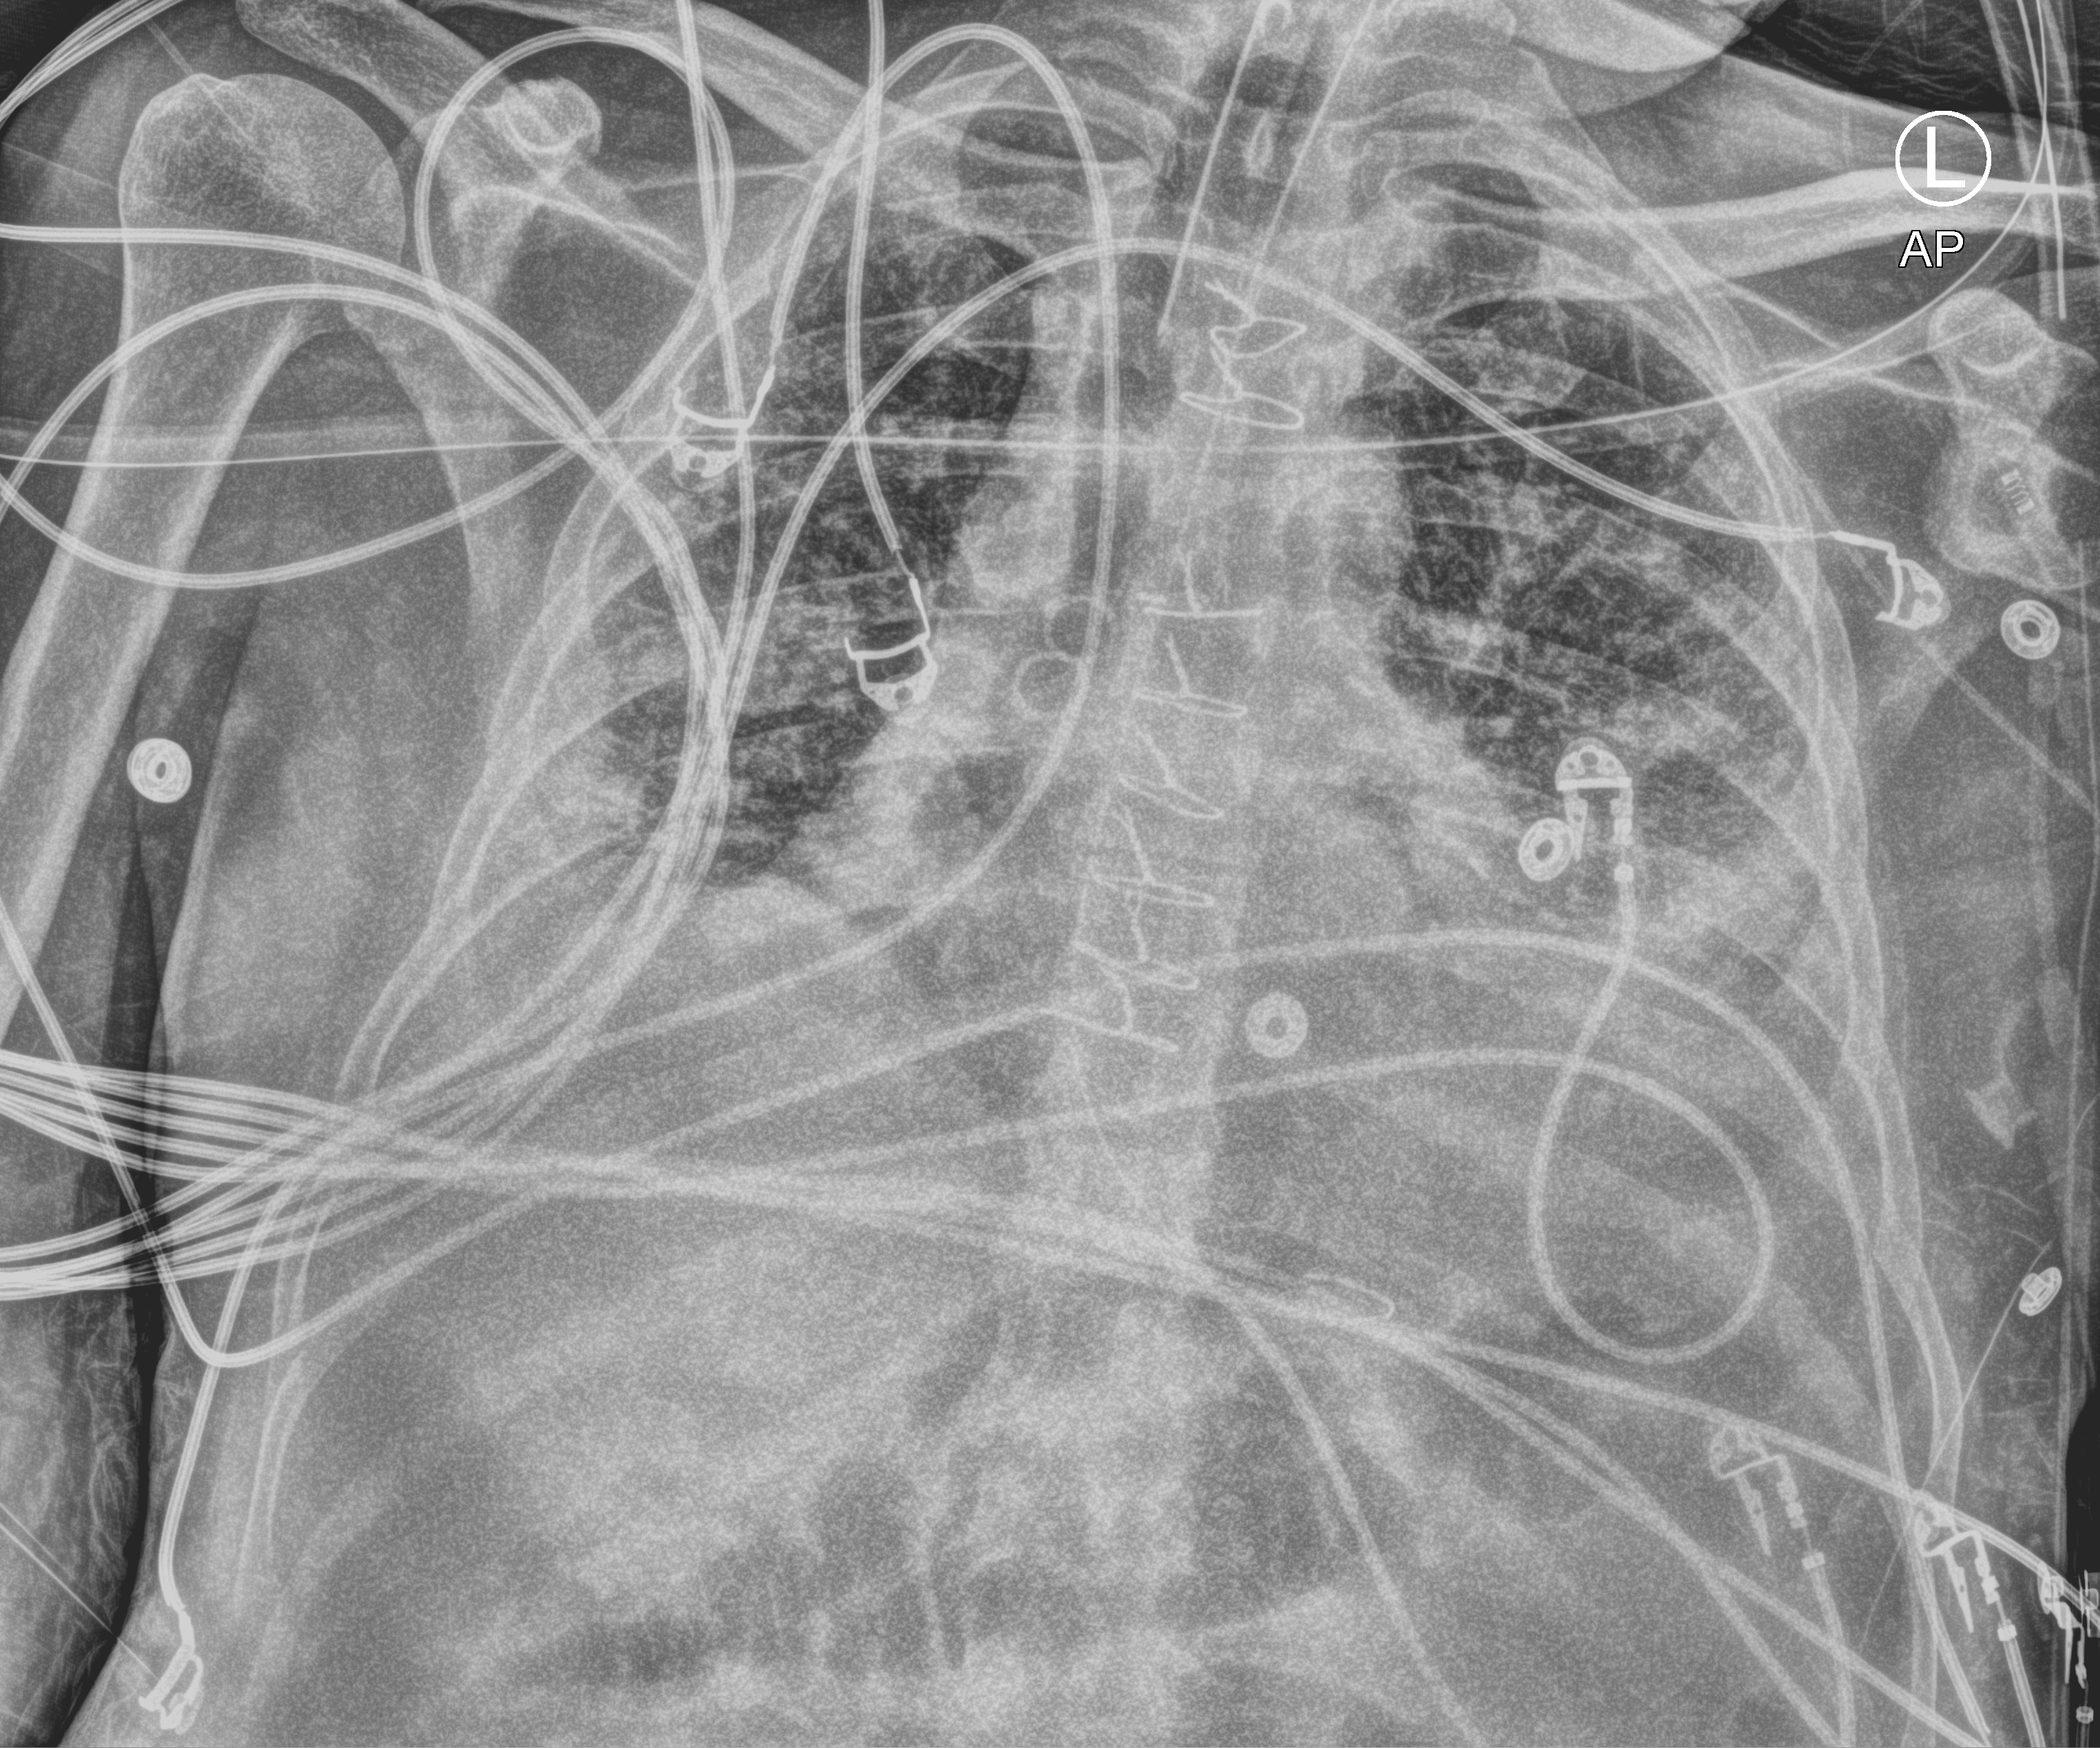
Bedside chest radiograph (computed radiography), anteroposterior (AP) projection. Patient hospitalised with COVID-19; male, aged 18–59 years.
Hospital-stay facts (about this admission, not read from this image; timing relative to this image not recorded):
- admitted to intensive care during this hospital stay: yes